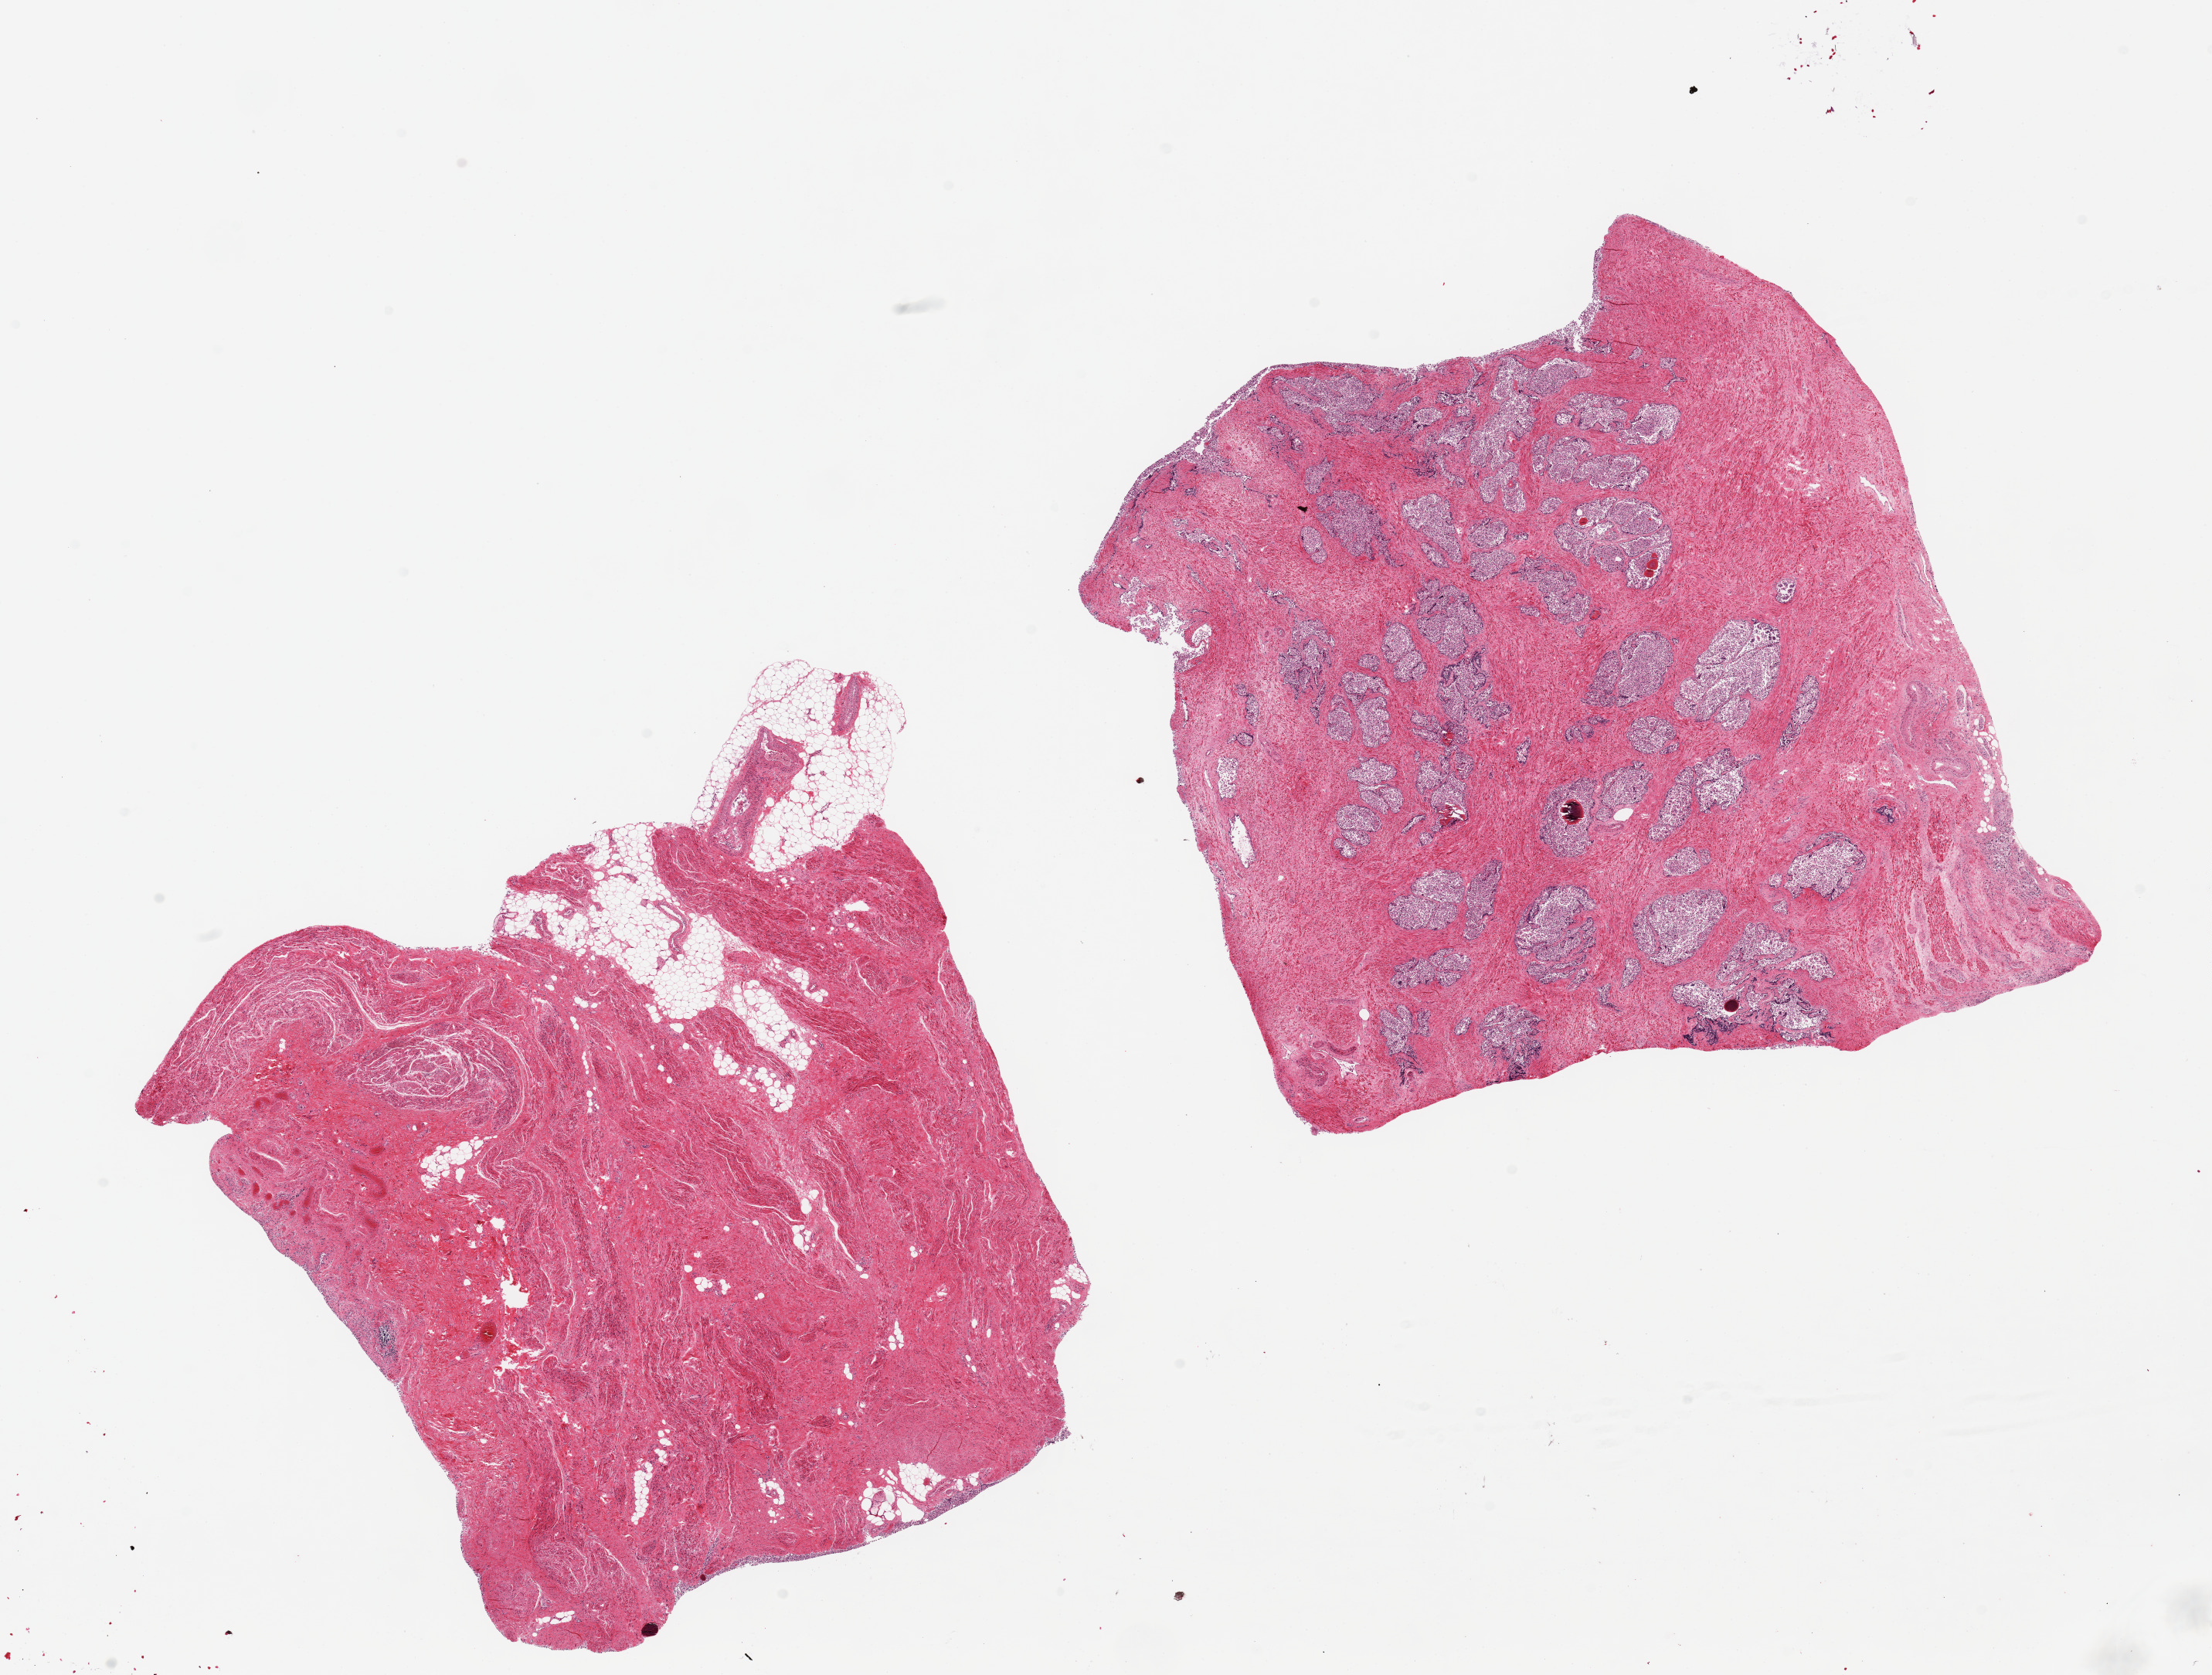
Digitized H&E-stained section — whole scanned area (about 22.6 x 17.1 mm) shown as a low-resolution overview; PAXgene-fixed paraffin-embedded (PFPE) section; target tissue: prostate; donor tissue sample. Donor sex: male.
- pathologist's review note for this sample: 2 pieces ~8x8mm, glands badly autolyzed; one aliquot essentially all fibromuscular stroma